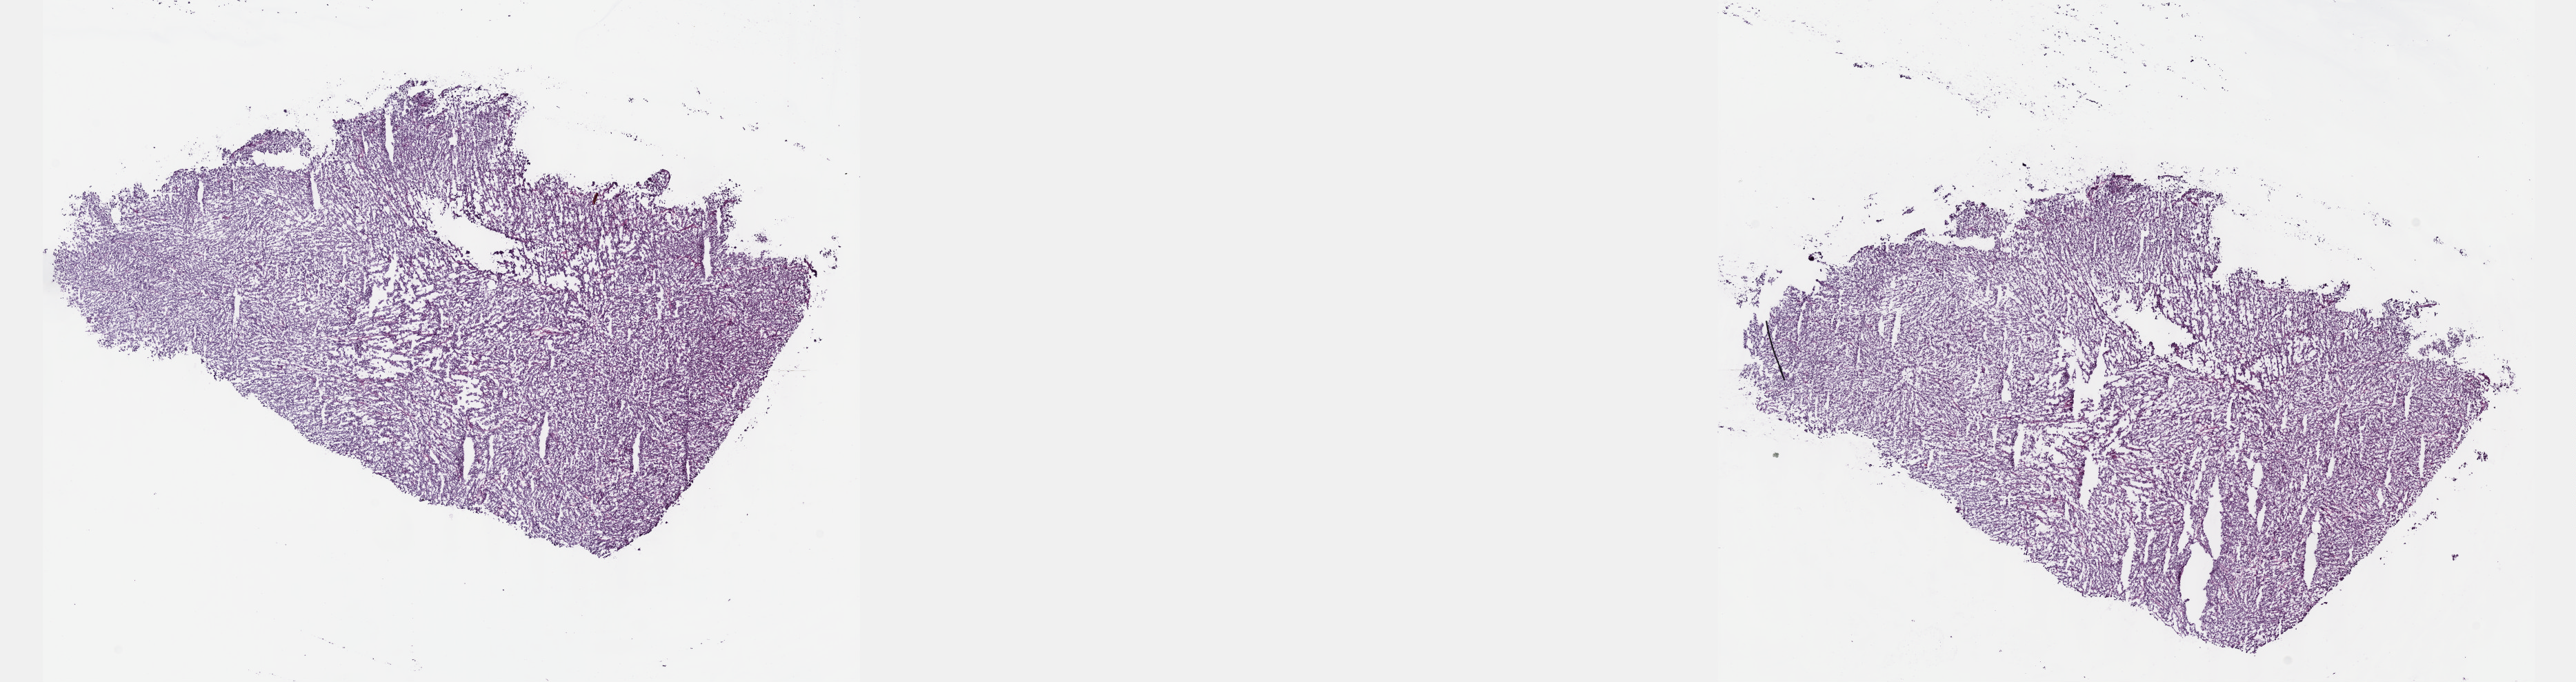
H&E whole-slide image — shown as a low-resolution overview of the whole scanned area (about 30.2 x 8.0 mm, slide scanned at 40x), frozen section, metastatic tumour sample. Patient: female, age at initial diagnosis 54 years. Pathologist review of this section (percent, as recorded): tumour cells 100%, tumour nuclei 92%, normal cells 0%, stromal cells 0%, necrosis 0%. Infiltration values recorded for this section: lymphocyte infiltration 0%, monocyte infiltration 0%, neutrophil infiltration 0%.
This section: metastatic tumour tissue. Patient diagnosis: Malignant melanoma, NOS.